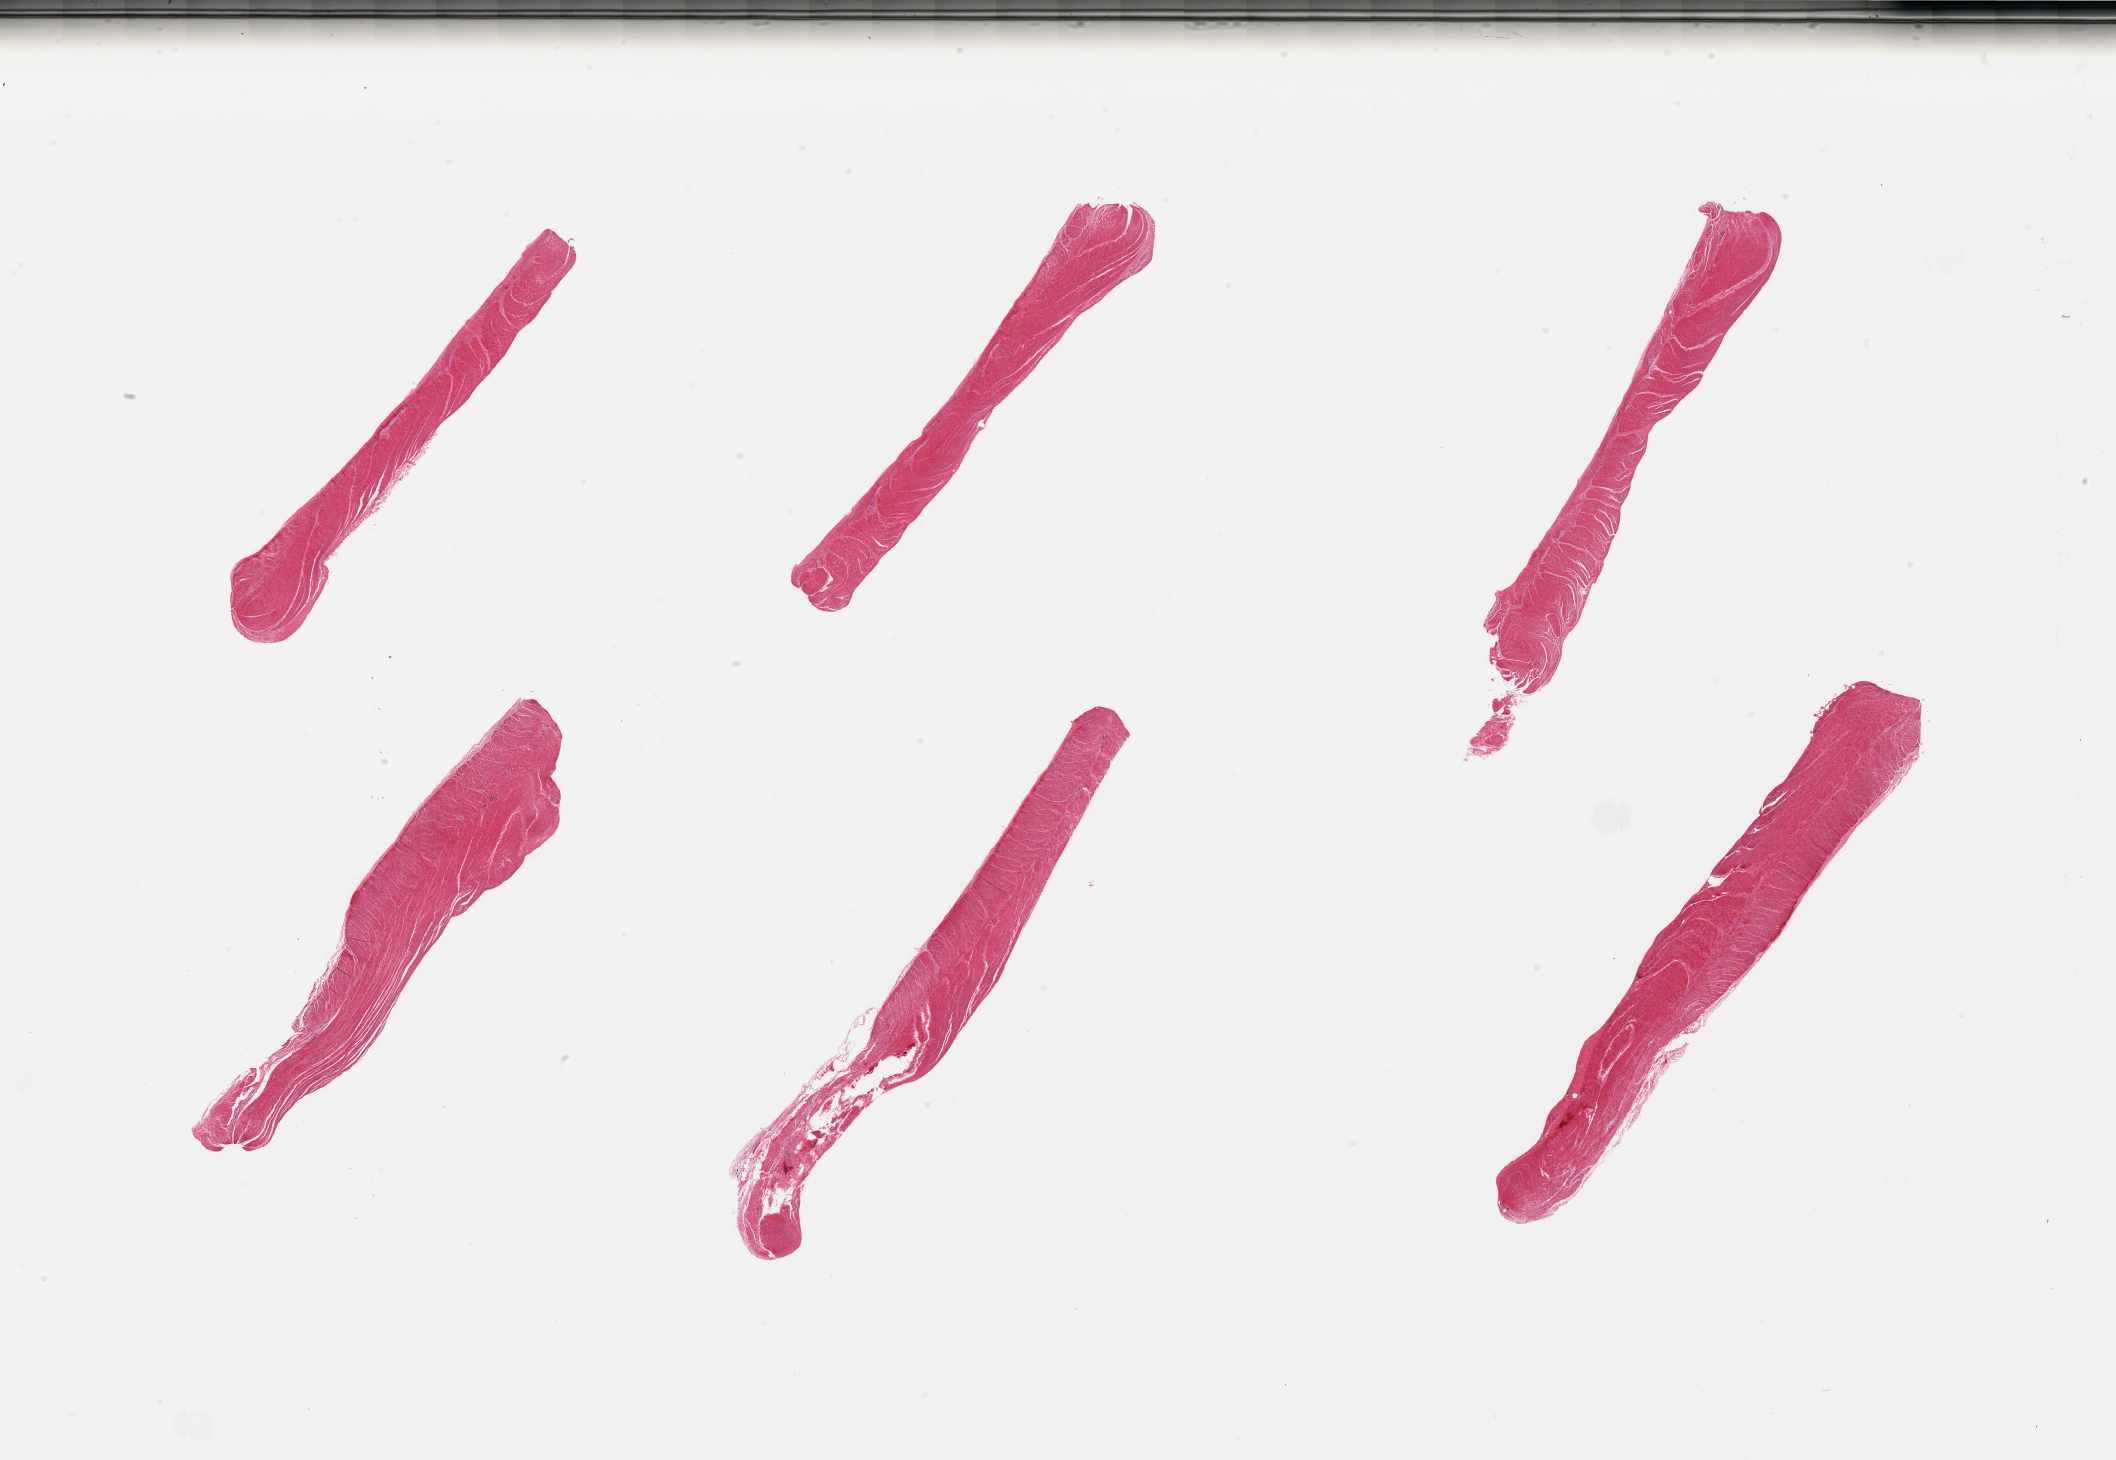
Whole-slide image, H&E stain, brightfield — a low-resolution overview of the entire scanned area, about 33.5 x 23.1 mm (from a 20x scan). PAXgene-fixed paraffin-embedded (PFPE) section. Section of sigmoid colon (target tissue). Tissue donor sample. Donor sex: male.
Pathologist's review note for this sample: 6 pieces; well dissected muscle.